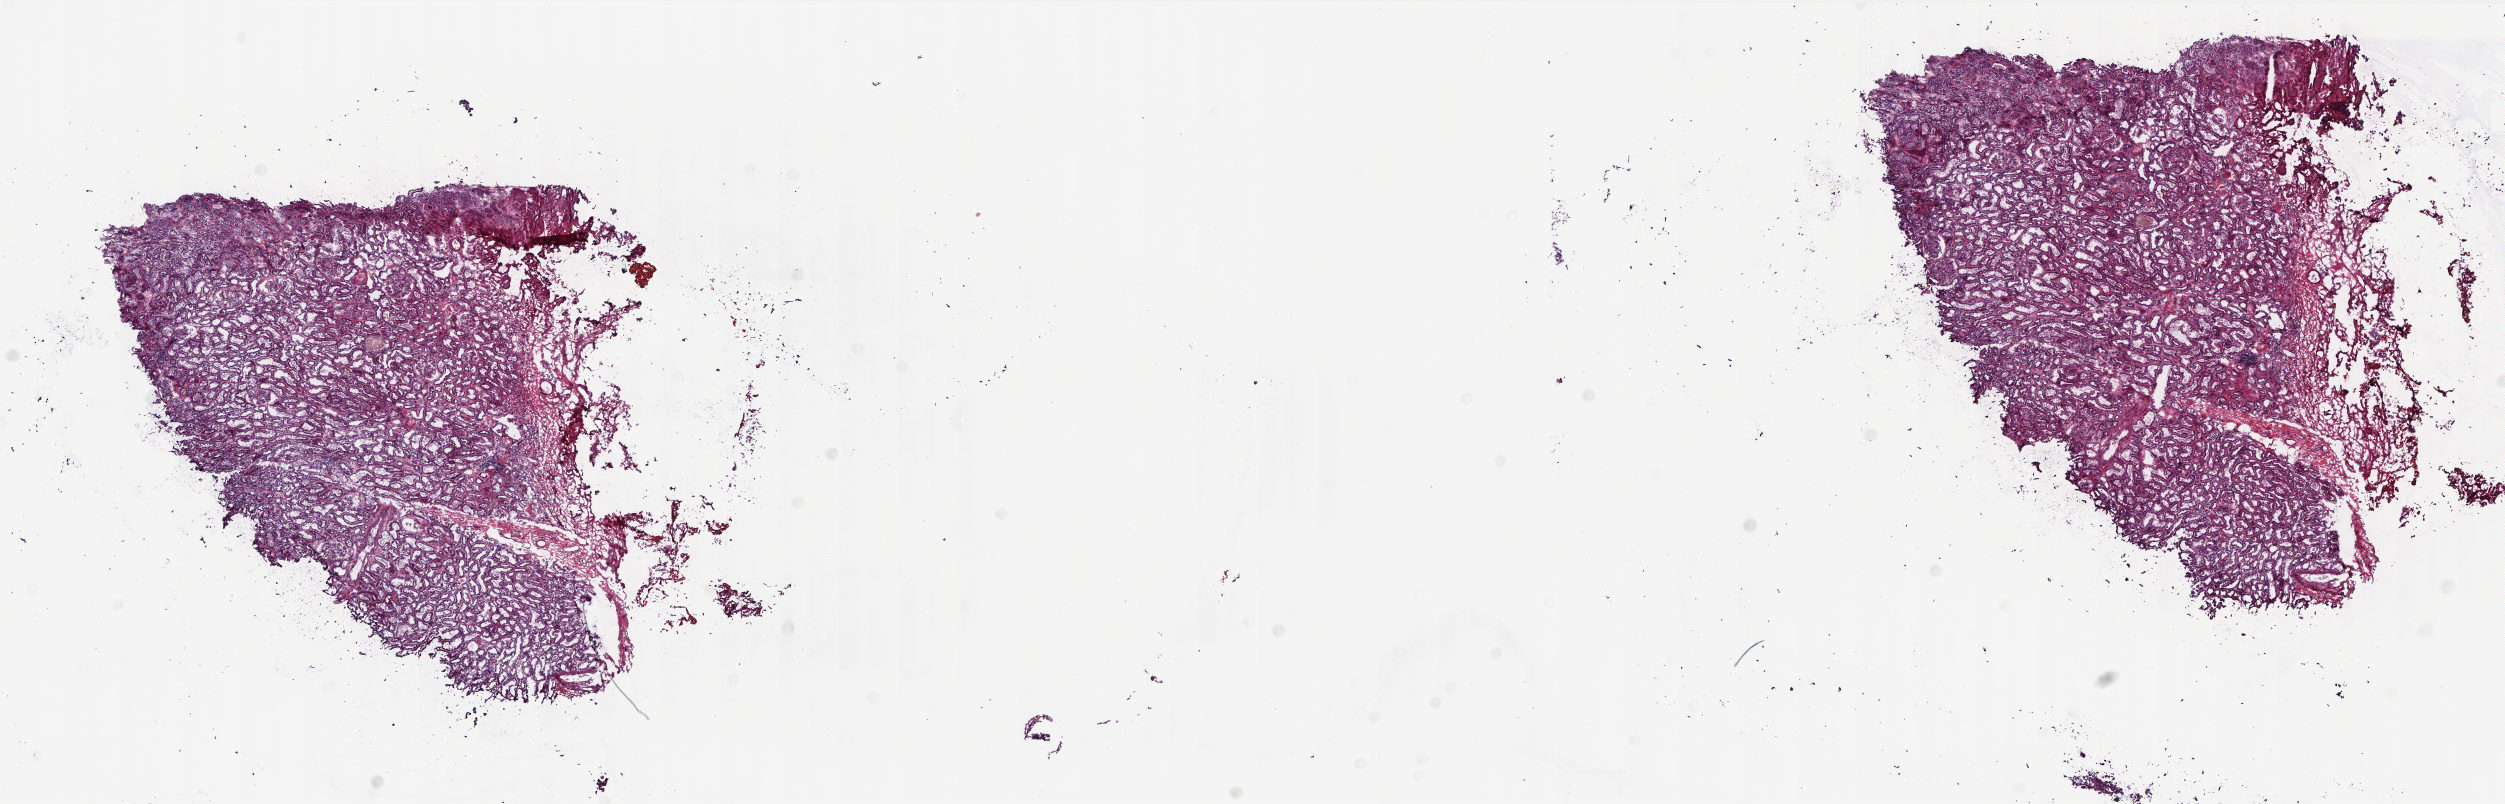
Digitized H&E tissue section (whole slide), whole scanned area (about 20.2 x 6.5 mm, slide scanned at 20x) shown as a low-resolution overview, frozen section from the top of the tissue portion, kidney, solid tissue normal (non-tumour tissue) sample. Female patient; age at initial diagnosis 74 years. Pathologist review of this section (percent, as recorded): tumour cells 0%, tumour nuclei 0%, normal cells 90%, stromal cells 10%, necrosis 0%. Inflammatory infiltration, as recorded: lymphocyte infiltration 0%, monocyte infiltration 0%, neutrophil infiltration 0%.
- this section: solid tissue normal sample (biorepository sample class)
- patient diagnosis: Papillary adenocarcinoma, NOS